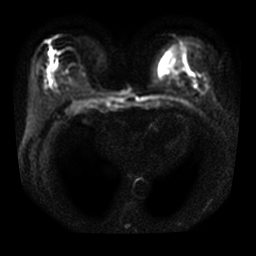
Breast MRI, one axial slice. Position 17 of 33 along the scan axis. Diffusion-weighted series; image 2 of 4 stored at this slice position (different b-values; order by instance number). 3 T. 5 mm slice thickness. 256 × 256 image matrix, field of view 320 × 320 mm. Female patient.
Annotated regions visible in this slice (expert manual segmentation):
- tumour on diffusion-weighted imaging: box from (x=186, y=60) to (x=189, y=70) px